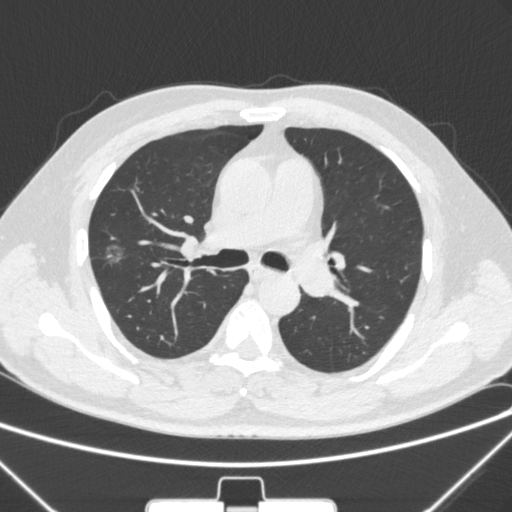
Chest CT, one axial slice; slice 193 of 320 in the series (ordered by position); lung window (W 1500 / L -600 HU); 1 mm slice thickness; 512 × 512 image matrix. Male patient, age 58 years. From the clinical record (not read from this slice): clinical TNM (as recorded): T1c N0 M0; histopathological grade: G2.
Outlined on this slice (bounding box drawn by a radiologist):
- lung tumour (recorded histology: adenocarcinoma): box from (x=97, y=237) to (x=129, y=277) px